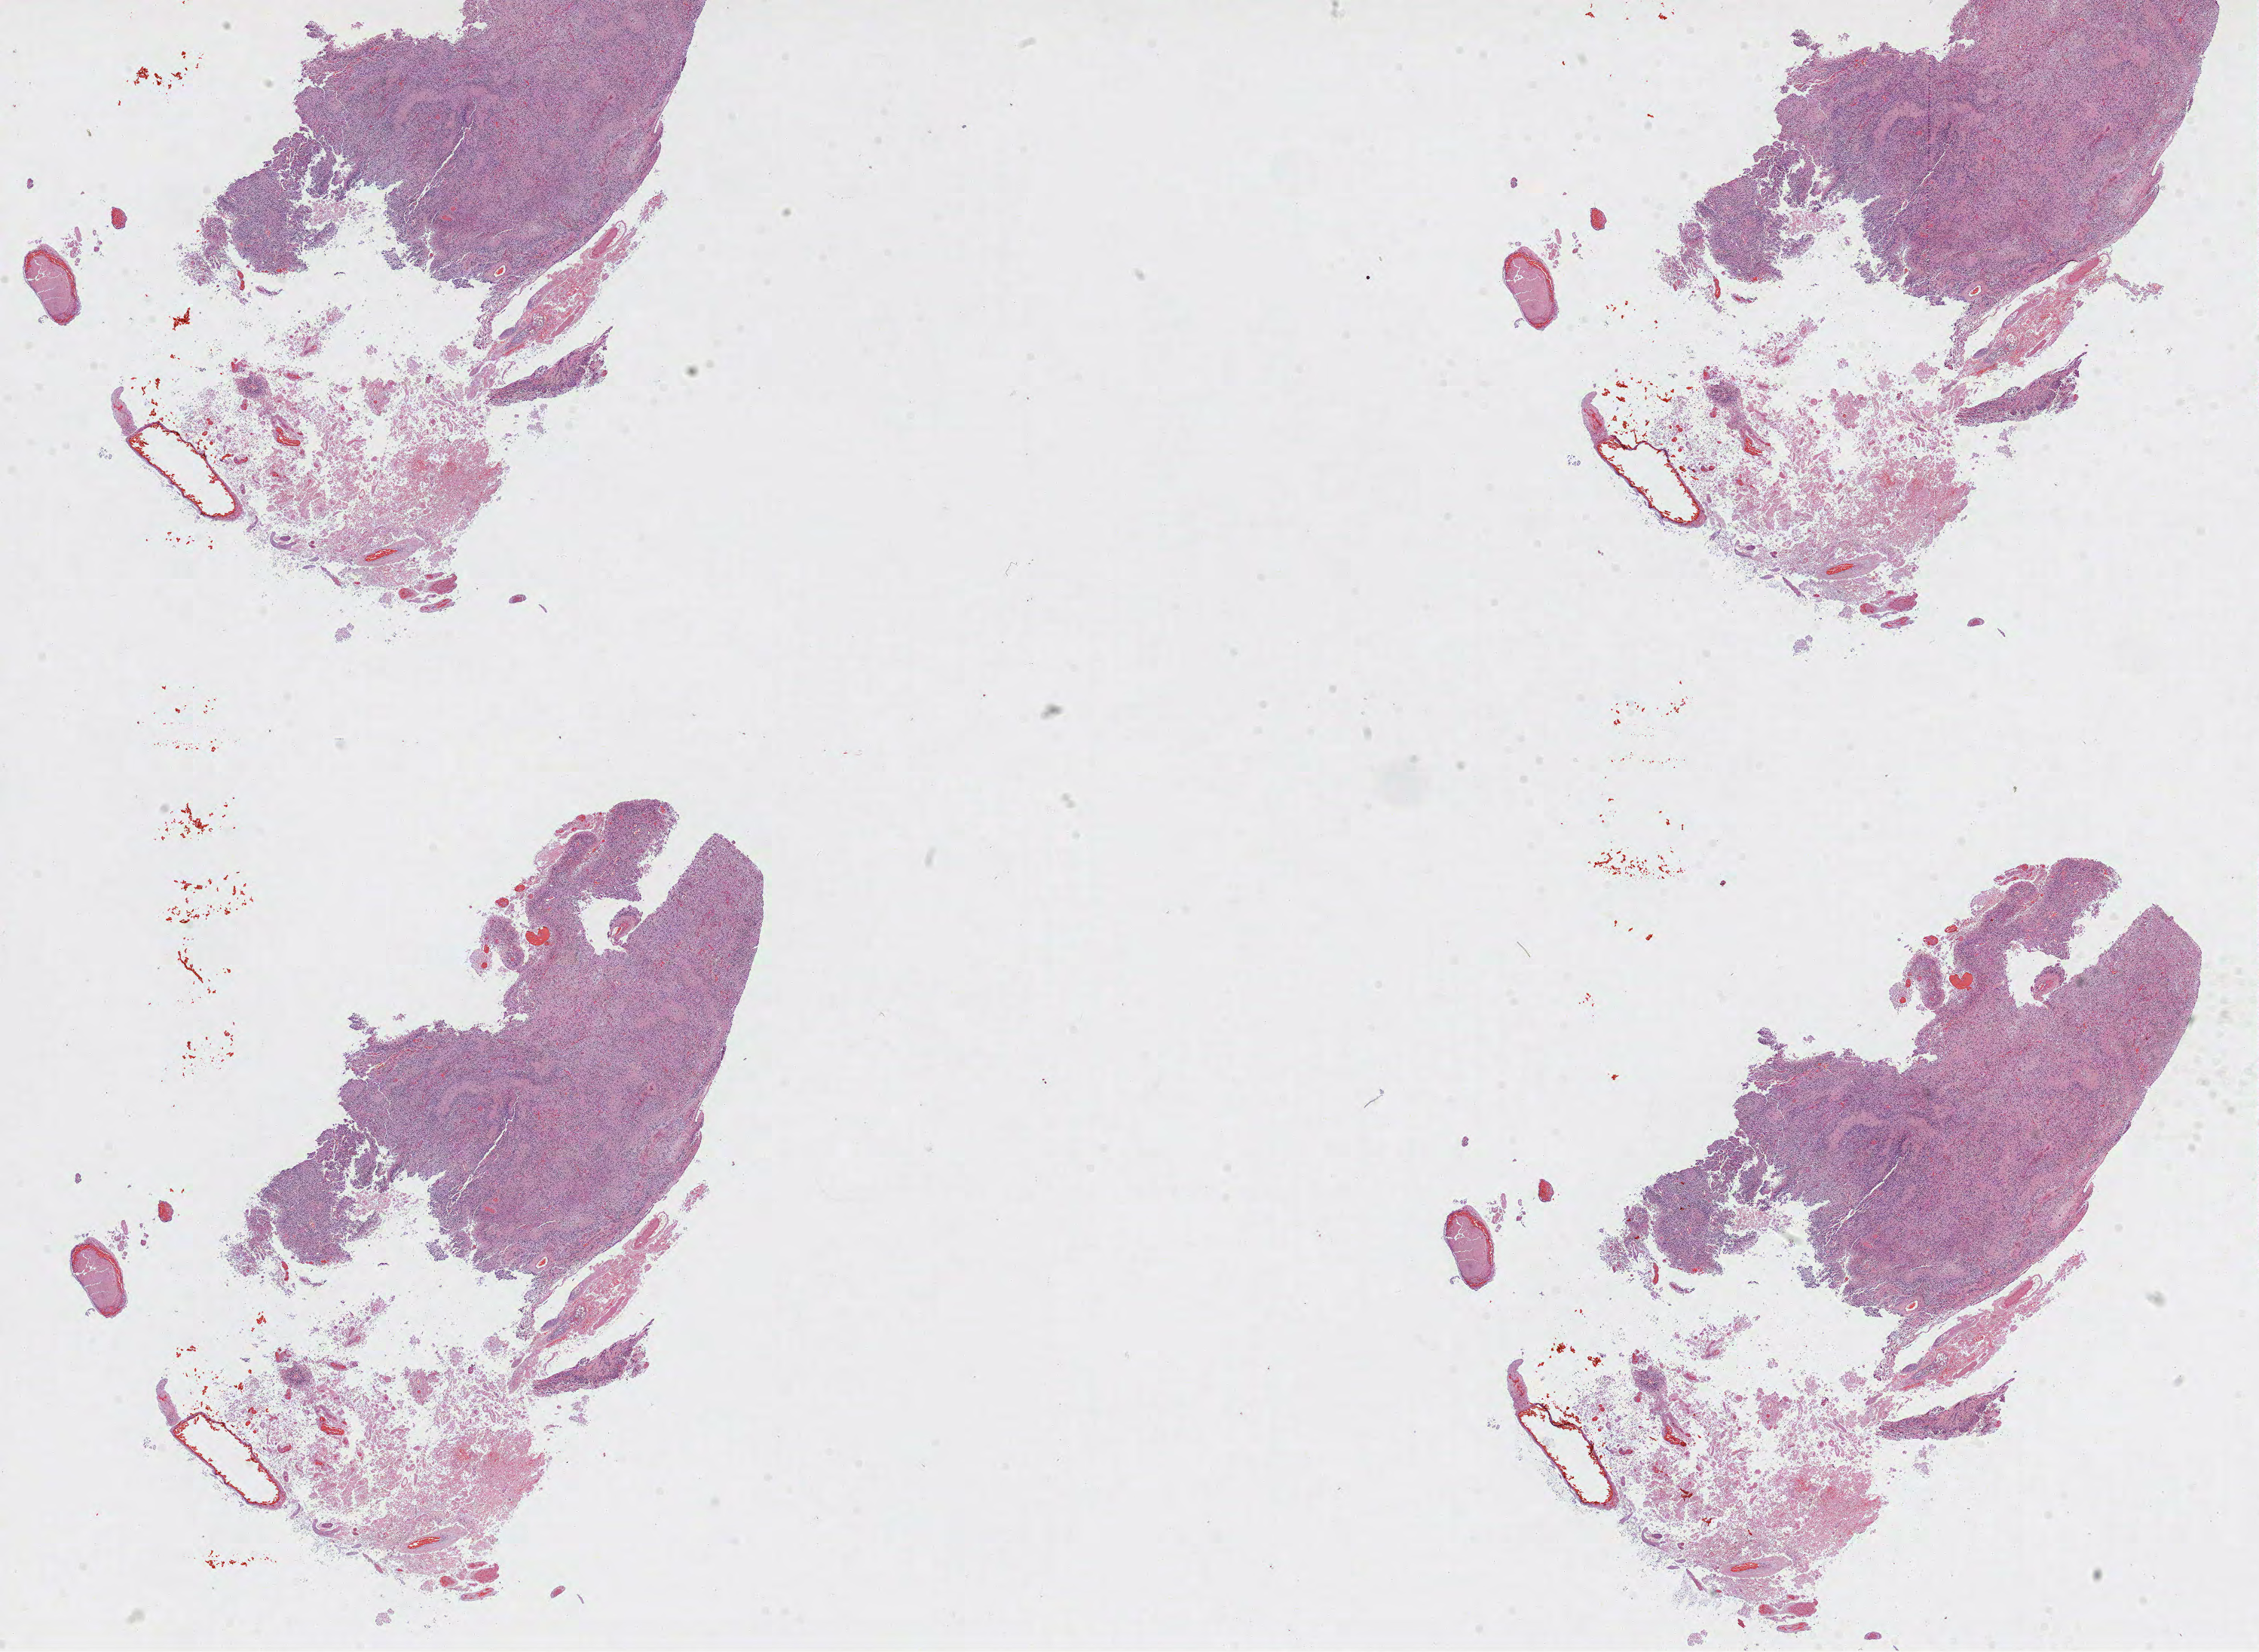
Digitized H&E-stained tissue section (whole slide), whole scanned area (about 24.2 x 17.7 mm, slide scanned at 40x) shown as a low-resolution overview. Formalin-fixed paraffin-embedded (FFPE) diagnostic section. Sample: primary tumour, brain. Female patient; age at initial diagnosis 64 years.
Pathologic diagnosis: Glioblastoma.